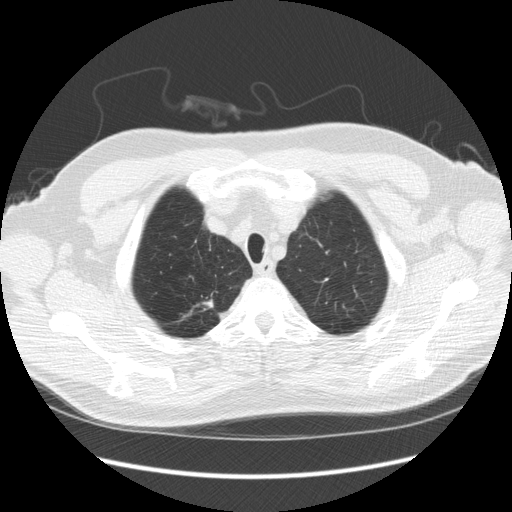
Axial slice from a low-dose chest CT screening exam, third annual screen, lung window (W 1500 / L -600 HU), 2.5 mm slice thickness, slice 27 of 248 in the series, 512 × 512 image matrix, field of view 380 × 380 mm. Male participant, aged 64 years at enrolment. Former smoker at enrolment.
Expert reader's lesion annotation, box from (x=179, y=287) to (x=227, y=325) px. The screening reader recorded 4 non-calcified nodules or masses ≥4 mm on this exam; which of them this box marks is not recorded. Official screen result: positive, other. Participant outcome: lung cancer diagnosed 15 days after this screen — adenocarcinoma, NOS, right upper lobe, moderately differentiated (G2), stage IA (AJCC 6th edition), 14 mm at pathology.